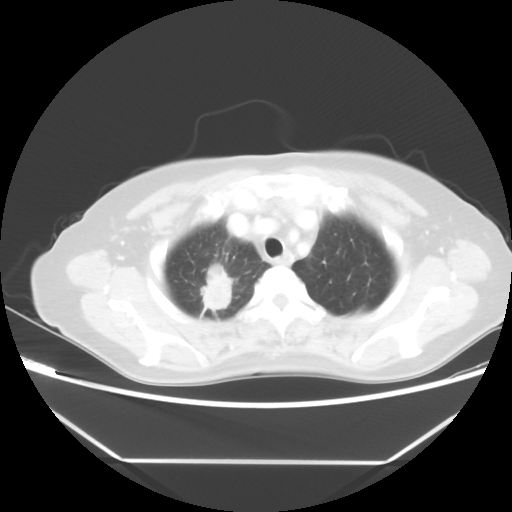
Chest CT, one axial slice; slice 42 of 48 in the series (ordered by position); lung window (W 1500 / L -600 HU); 5 mm slice thickness; 512 × 512 image matrix. Female patient, age 65 years. From the clinical record (not read from this slice): clinical TNM (as recorded): T1c N1 M1.
Outlined on this slice (rectangle marked by the reading radiologist):
- lung tumour (recorded histology: adenocarcinoma): bounding box (x1, y1, x2, y2) in pixels: (192, 261, 236, 317)